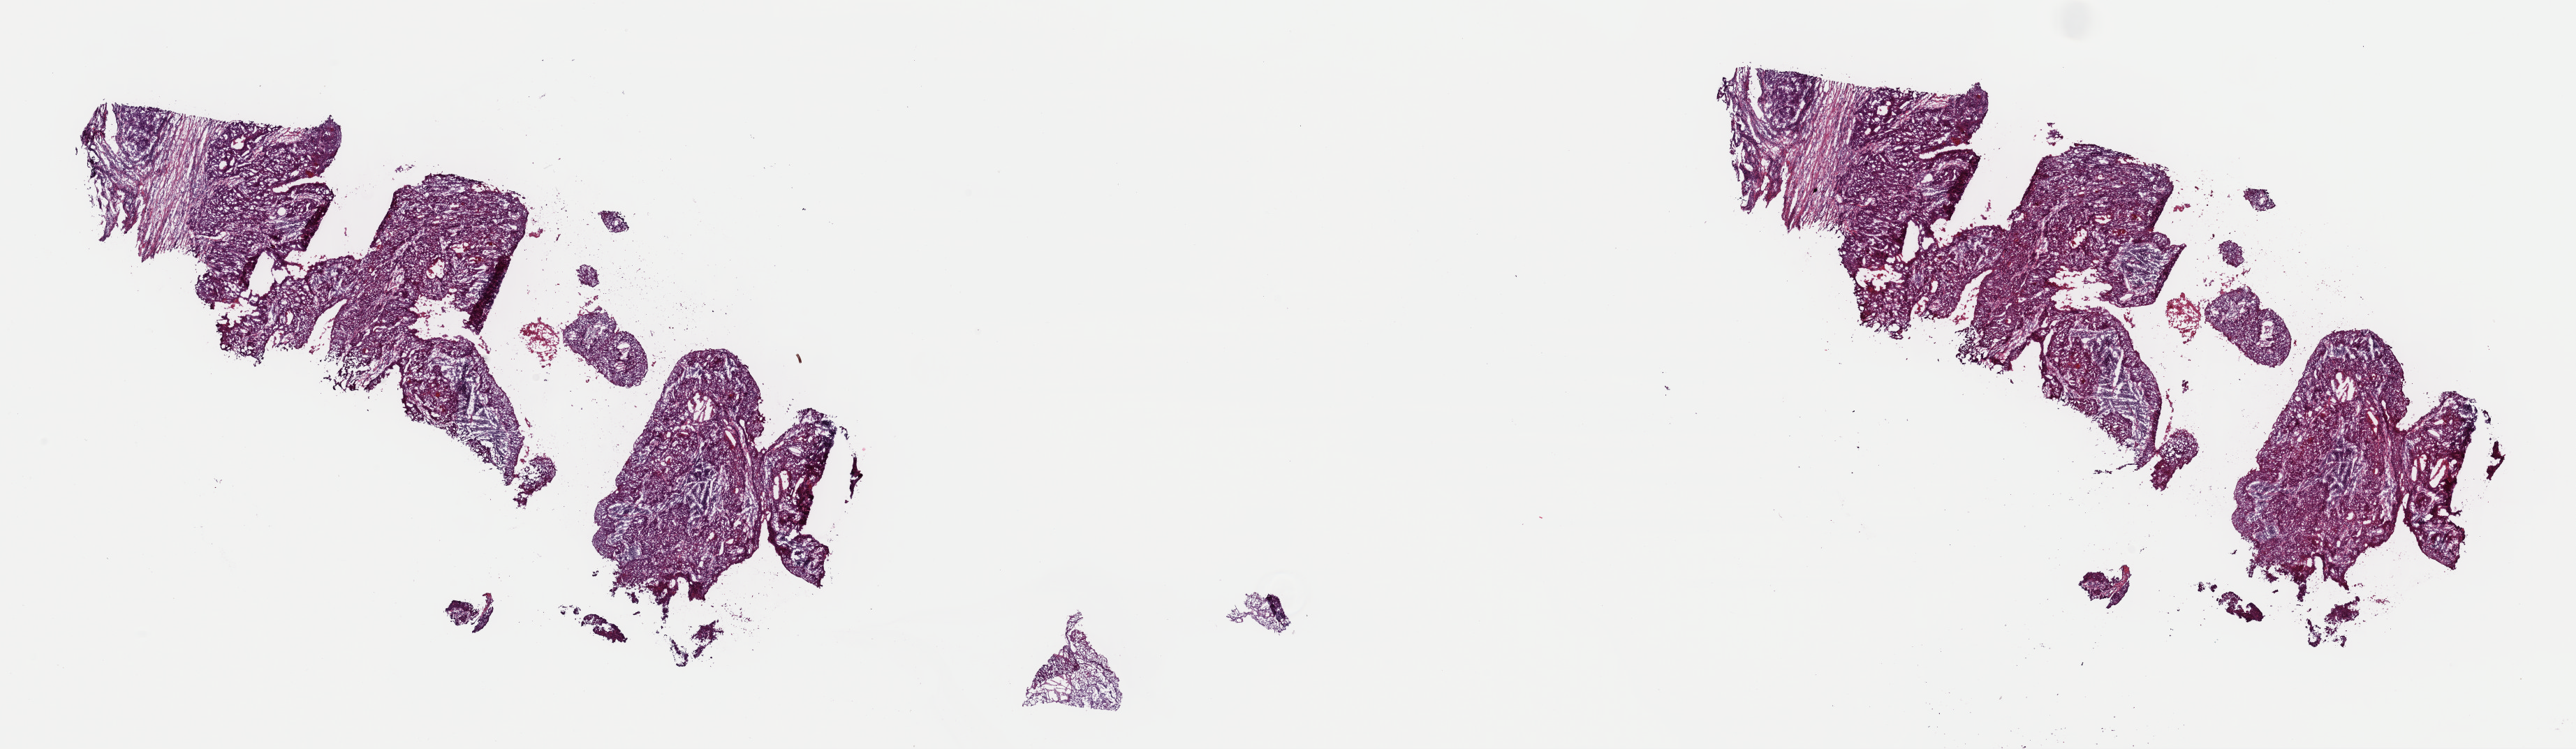
H&E whole-slide image, whole scanned area (about 29.1 x 8.5 mm, from a 40x scan) shown as a low-resolution overview, frozen section from the top of the tissue portion, metastatic tumour sample. Patient: female, age at initial diagnosis 55 years. Composition of this section per pathologist review: tumour cells 70%, tumour nuclei 75%, normal cells 0%, stromal cells 25%, necrosis 5%. Infiltration values recorded for this section: lymphocyte infiltration 15%, monocyte infiltration 3%, neutrophil infiltration 3%.
This section: metastatic tumour tissue. Patient diagnosis: Squamous cell carcinoma, NOS (primary site: tonsil, NOS).